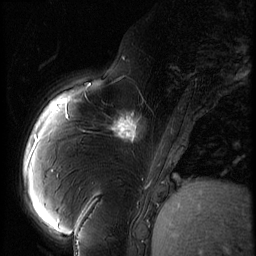
Breast MRI (dynamic contrast-enhanced), one sagittal slice; slice 17 of 60 in the series (ordered by position); 3 images stored at this slice position (order not interpretable as contrast timing); 1.5 T; TE 4.2 ms, TR 9 ms; 2.5 mm slice thickness; 256 × 256 image matrix, field of view 180 × 180 mm. Female patient, age 57 years. From the clinical record (not read from this slice): setting: breast cancer imaged before/during neoadjuvant chemotherapy; receptor status: triple-negative.
Outlined on this slice (semi-automatic segmentation, software-assisted and operator-edited):
- analysis volume of interest (the breast-tissue region the enhancement analysis was run in; not a lesion): bounding box <106,101,157,152> (left, top, right, bottom; pixels)
- tumour enhancement mask (voxels above the 140 % enhancement threshold inside the analysis volume of interest): <112,117,140,142>